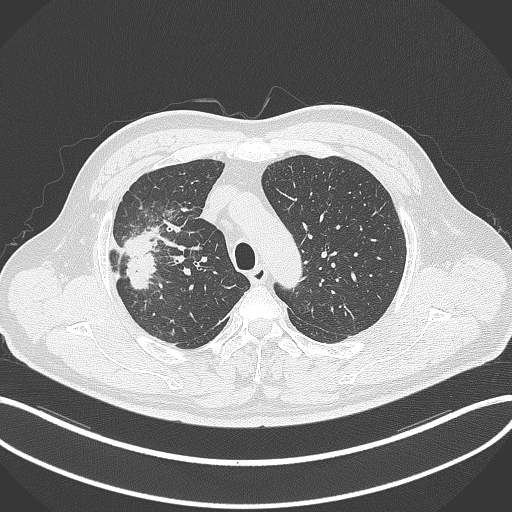
Chest CT, one axial slice. Slice 259 of 348 in the series (ordered by position). Reconstruction kernel B70f. 120 kVp. Lung window (W 1500 / L -600 HU). 1 mm slice thickness. 512 × 512 image matrix, field of view 400 × 400 mm. Male patient, age 55 years. From the clinical record (not read from this slice): clinical TNM (as recorded): T3 N2 M1.
Annotated regions visible in this slice (bounding box drawn by a radiologist):
- lung tumour (recorded histology: adenocarcinoma): bounding box <121,225,160,293> (left, top, right, bottom; pixels)